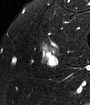
MRI of an extremity soft-tissue mass, one axial slice; slice 50 of 65 in the series (ordered by position); T2-weighted fat-saturated; MR volume resampled by the dataset authors to the PET/CT grid (not the native acquisition matrix); 3.27 mm slice thickness; 90 × 105 image matrix. Male patient. From the clinical record (not read from this slice): histological type: mixoid liposarcoma; grade: low; site of the primary tumour: left thigh.
Annotated regions visible in this slice (expert contour drawn on MRI and transferred to this co-registered scan by the dataset authors):
- gross tumour volume (mass): bounding box [x1, y1, x2, y2] px = [39, 43, 56, 56]